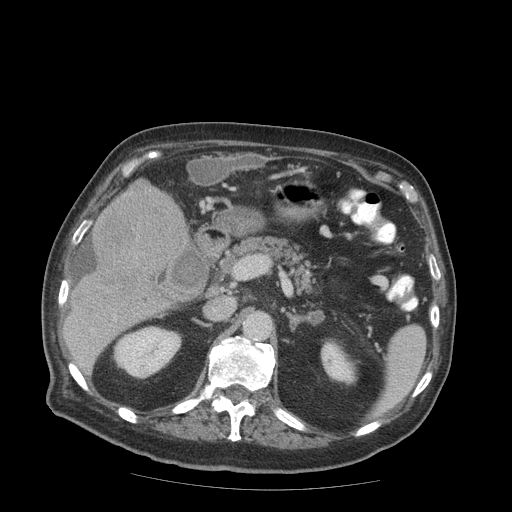
Contrast-enhanced abdominal CT (liver protocol), one axial slice. Slice 39 of 99 in the series (ordered by position). Reconstruction kernel STANDARD. 140 kVp. Soft-tissue window (W 400 / L 40 HU). 2.5 mm slice thickness. 512 × 512 image matrix. From the clinical record (not read from this slice): diagnosis: hepatocellular carcinoma (patient treated with transarterial chemoembolisation; whether this scan precedes or follows treatment is not stated here); TNM stage (as recorded): Stage-IIIB; Child-Pugh class: A.
Structures marked on this image (semi-automatically segmented with operator editing):
- liver parenchyma outside the tumour (the mass and vessels are separate outlines, so this box may not span the whole liver): box from (x=66, y=184) to (x=202, y=342) px
- mass: (x=77, y=179)–(x=189, y=314)